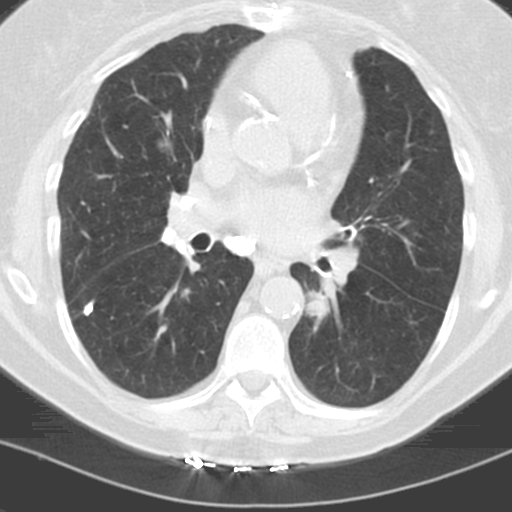
Low-dose screening chest CT, one axial slice; position 58 of 121 along the scan axis; 120 kVp; lung window (W 1500 / L -600 HU); 512 × 512 image matrix, field of view 278 × 278 mm.
Outlined on this slice (outlined manually by an expert reader):
- lesion 2 (tumor, lower lobe of left lung): bounding box <308,299,329,317> (left, top, right, bottom; pixels)